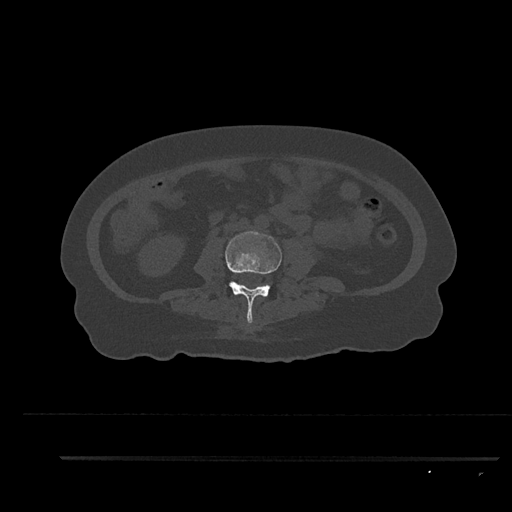
CT including the spine, one axial slice; slice 78 of 797 in the series (ordered by position); reconstruction kernel Br40s/3; 120 kVp; bone window (W 1800 / L 400 HU); 0.5 mm slice thickness; 512 × 512 image matrix. Patient: female, 44 years. Case-level facts recorded for this patient, not image findings: primary cancer: renal; vertebrae with lytic lesions (as recorded): L1.
Annotated regions visible in this slice (semi-automatically segmented with operator editing):
- L3 vertebra: bounding box (x1, y1, x2, y2) in pixels: (225, 231, 282, 324)